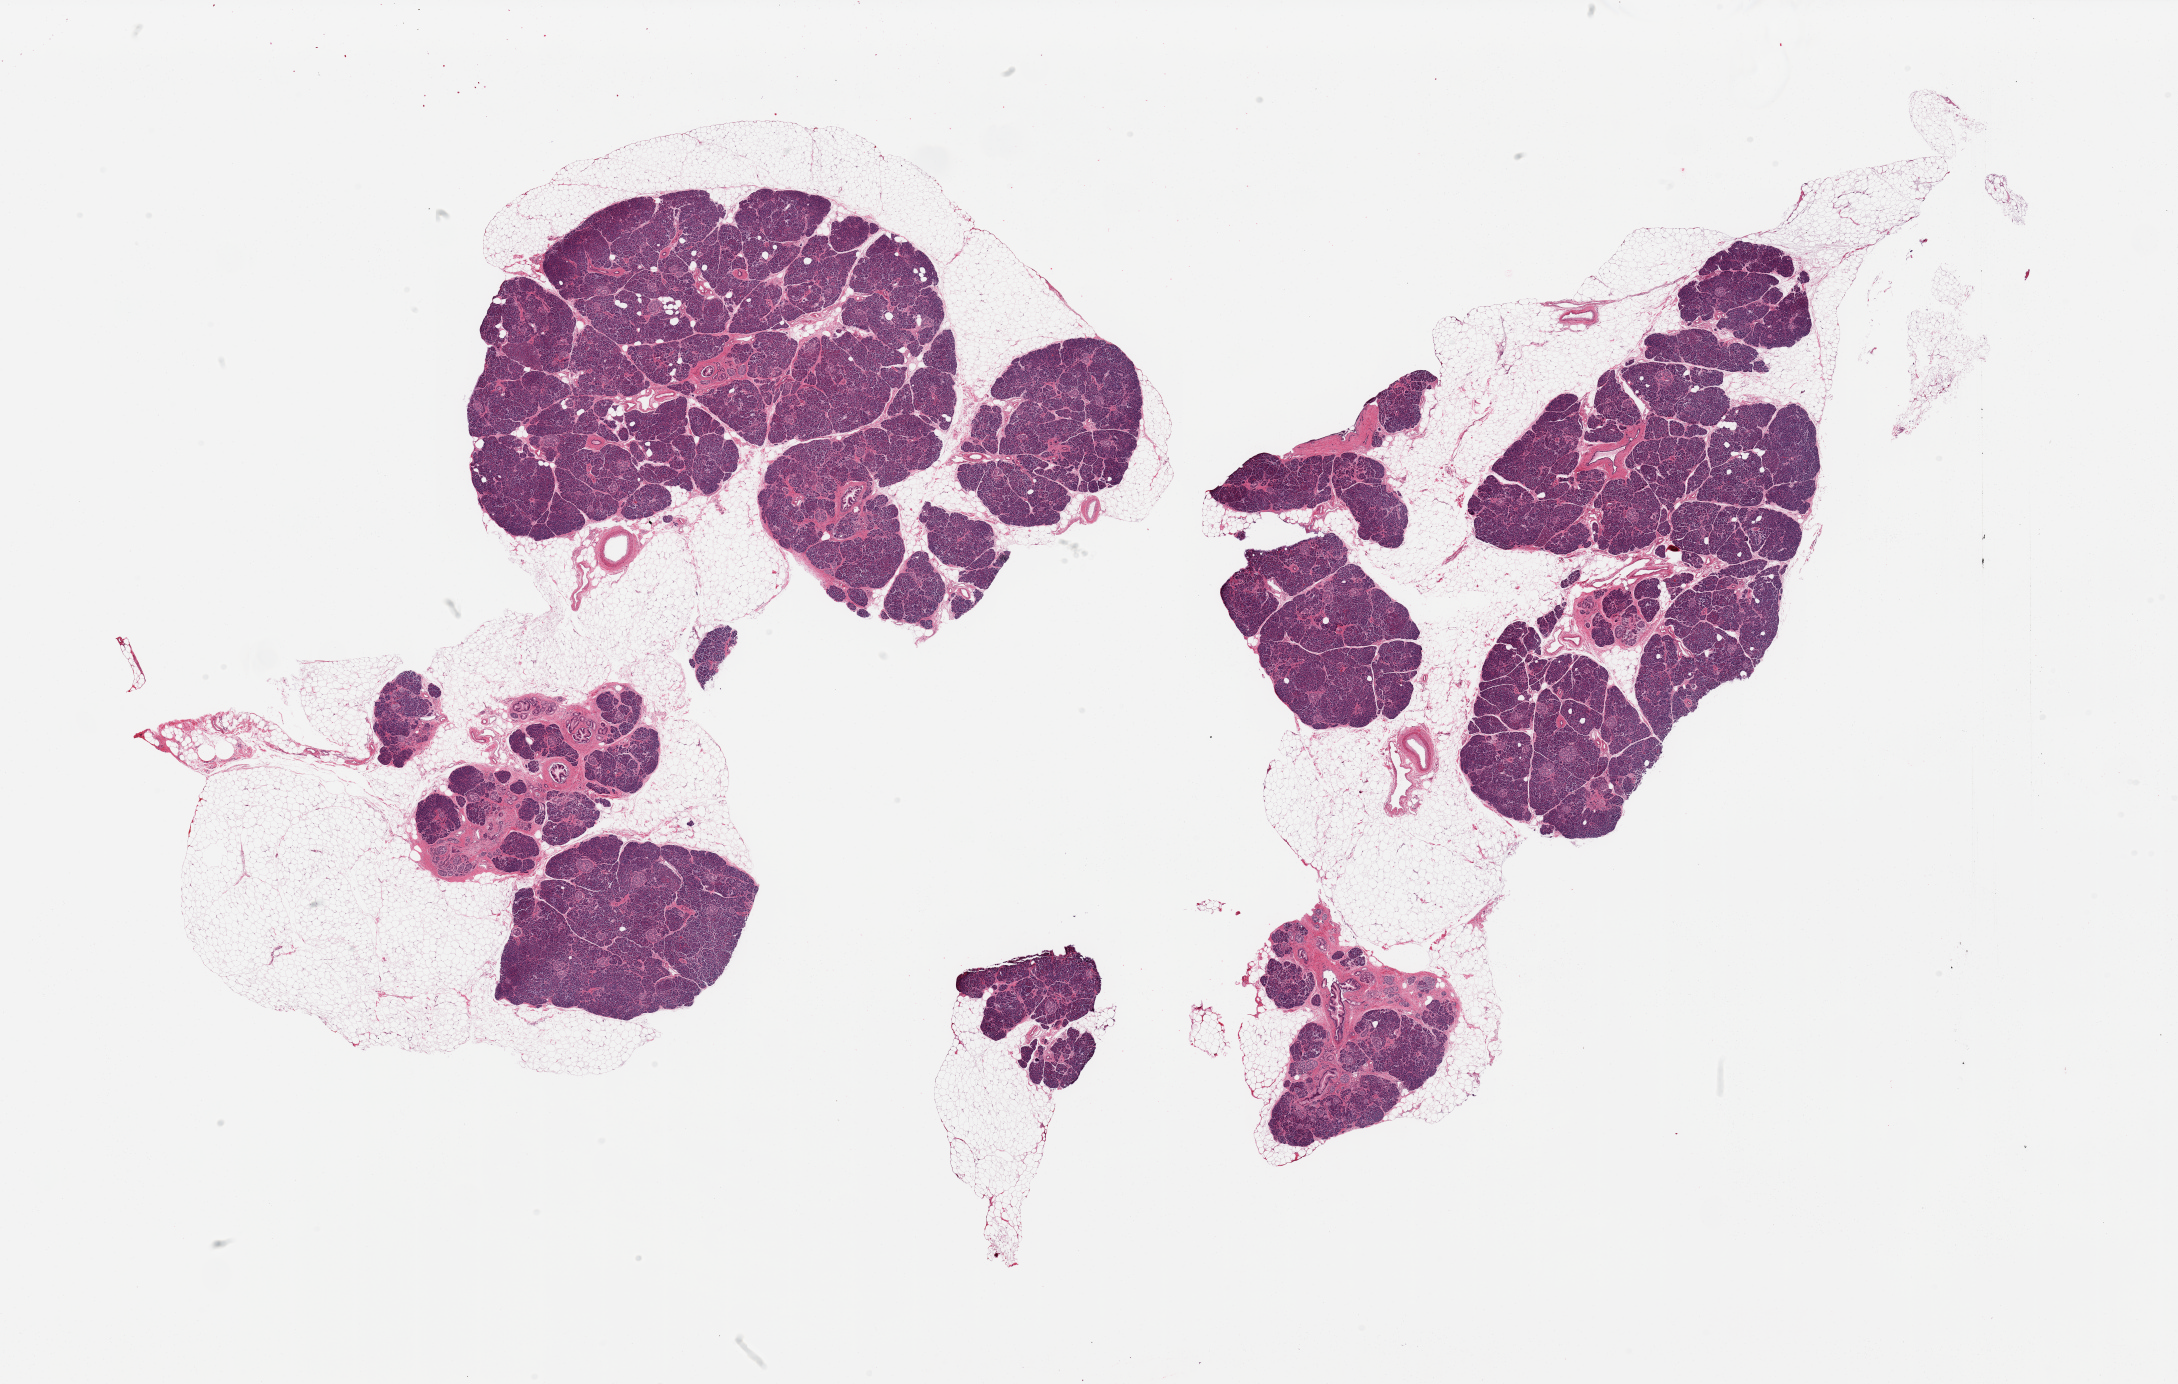
Whole-slide image, hematoxylin and eosin (H&E) stain, whole scanned area (about 34.5 x 21.9 mm) shown as a low-resolution overview. PAXgene-fixed, paraffin-embedded tissue. Section of pancreas (target tissue). Donor tissue sample.
Reviewer comment on this tissue sample: 2 pieces; up to 50% of both is fat, numerous islets, PanIN 1B.